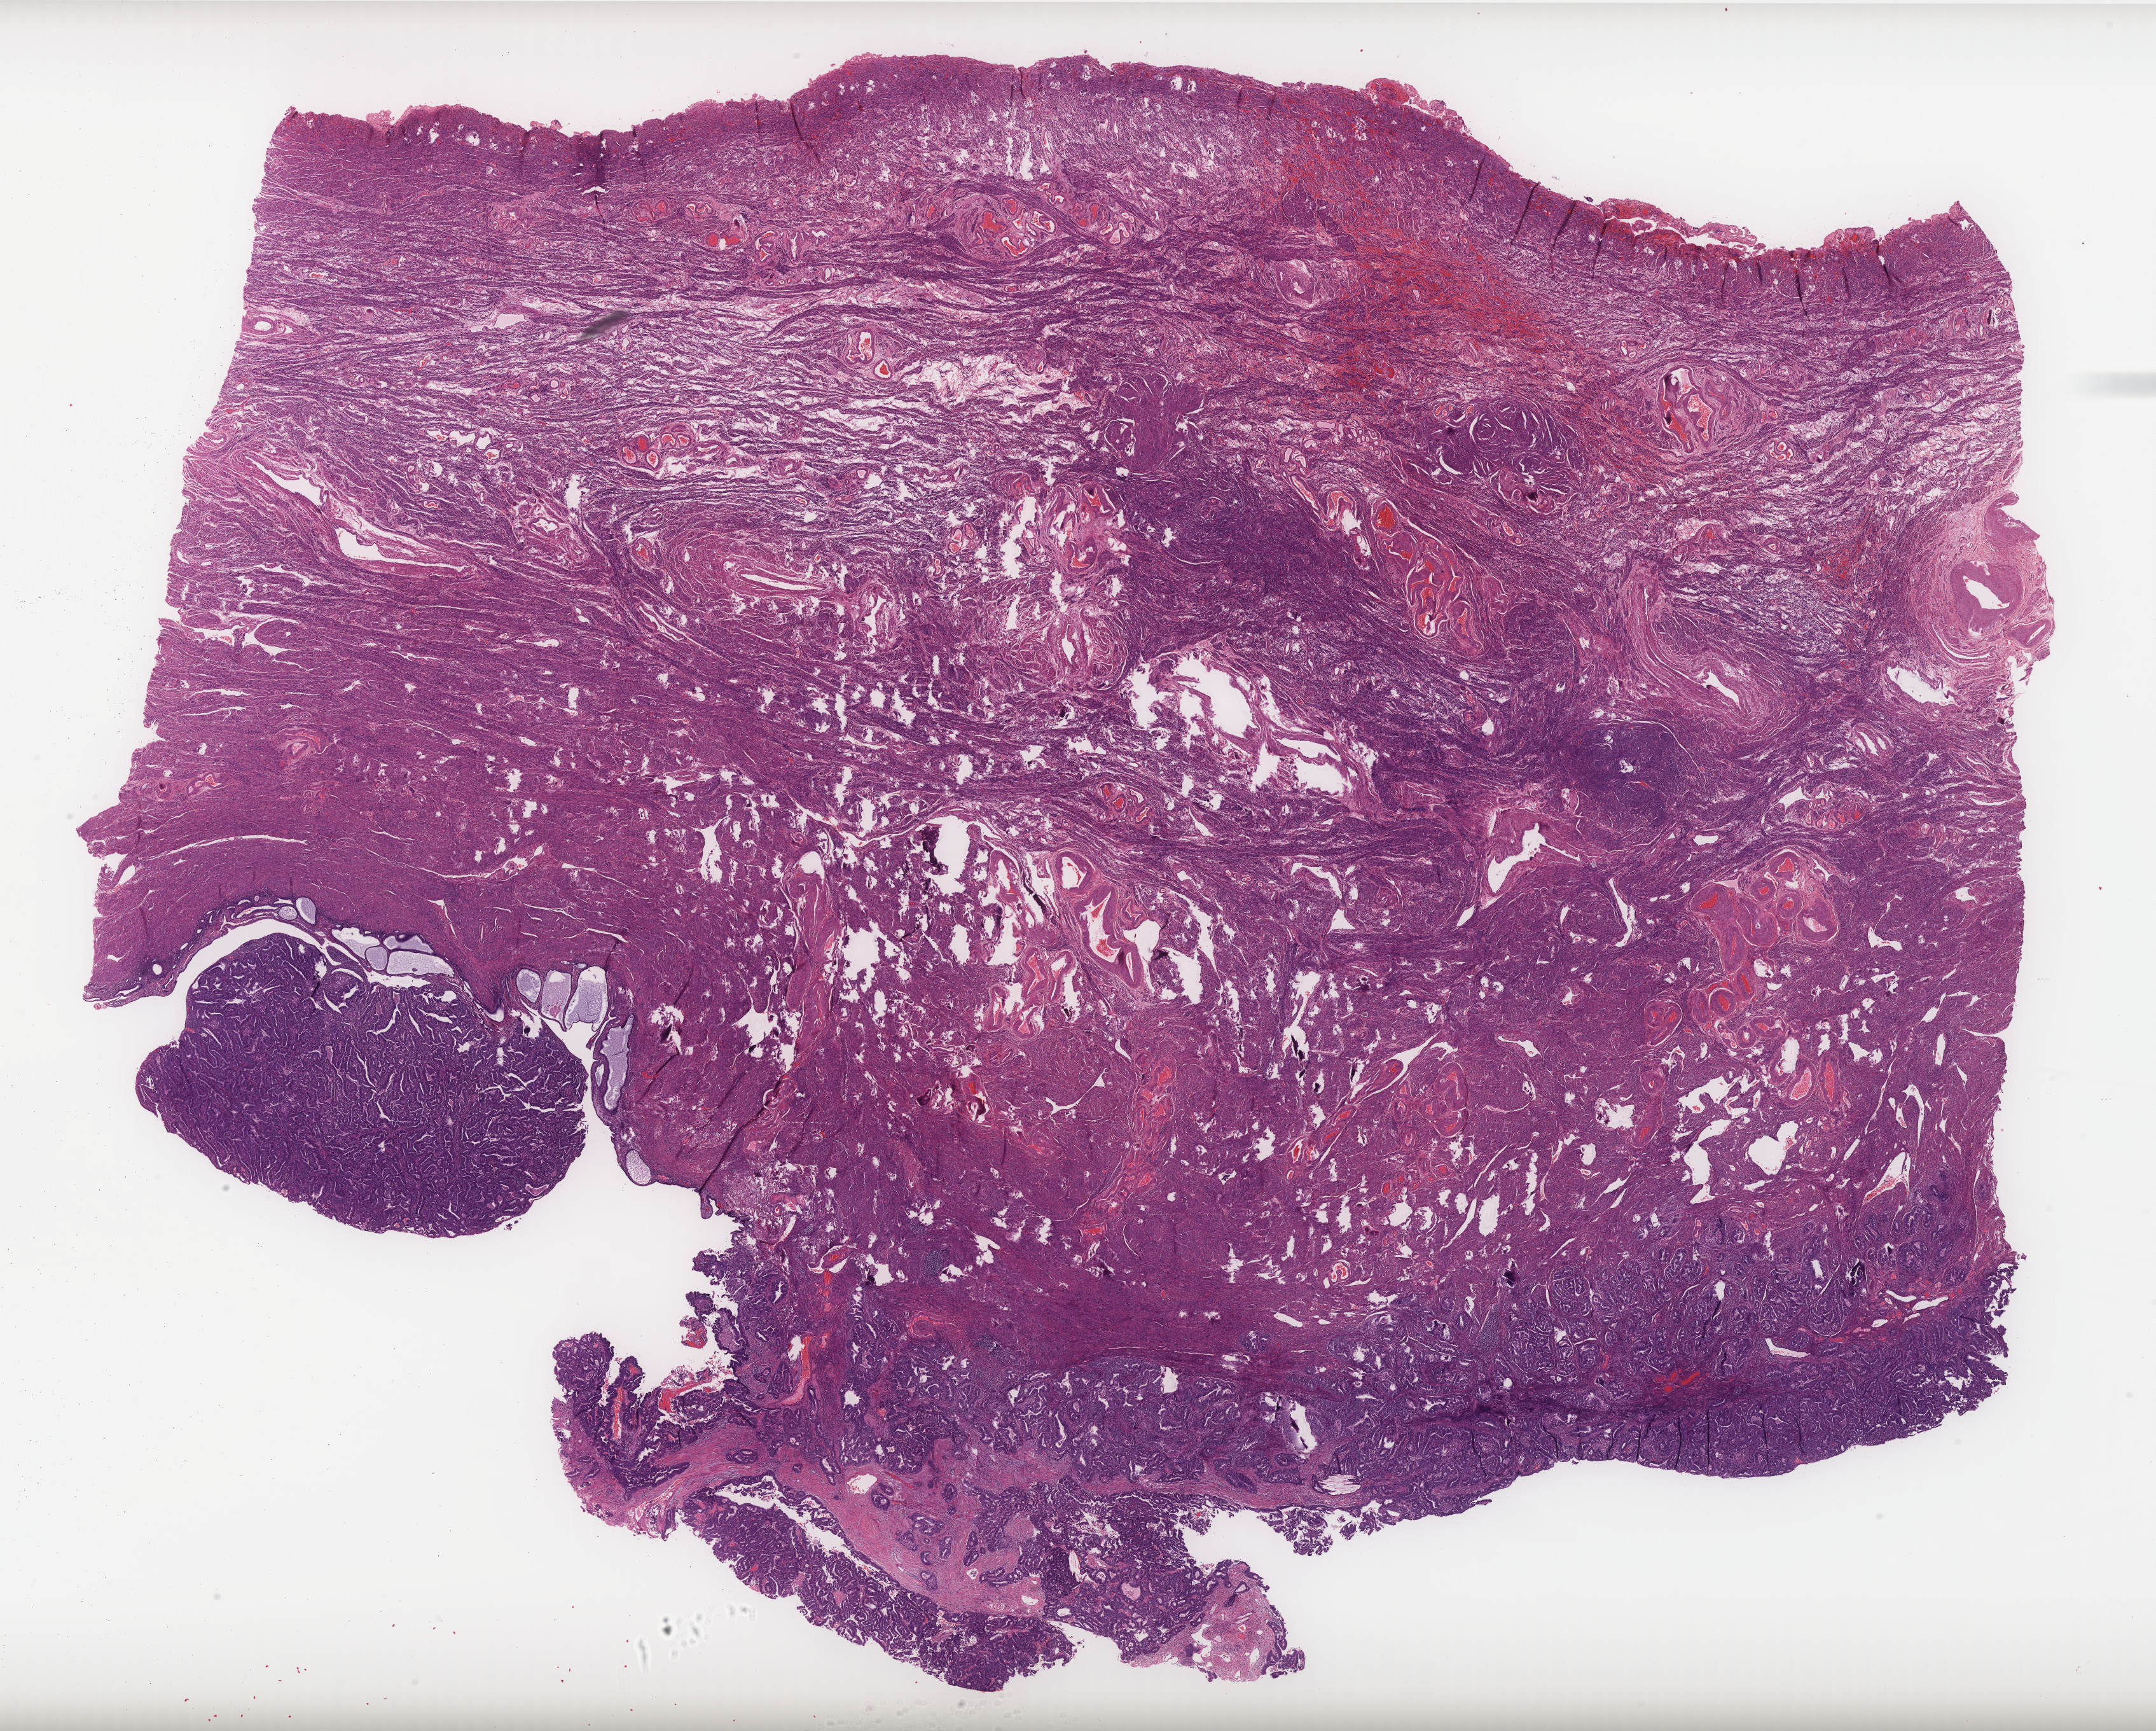
Whole-slide histology image, Hematoxylin and eosin (H&E) stained — low-resolution overview of the scanned area, about 27.2 x 21.8 mm. FFPE section. Uterus, primary tumour sample. Female, age 65 years at initial diagnosis. Histologic grade: G1 (well differentiated).
FIGO stage: IB. Pathologic diagnosis: Endometrioid adenocarcinoma, NOS (endometrium).